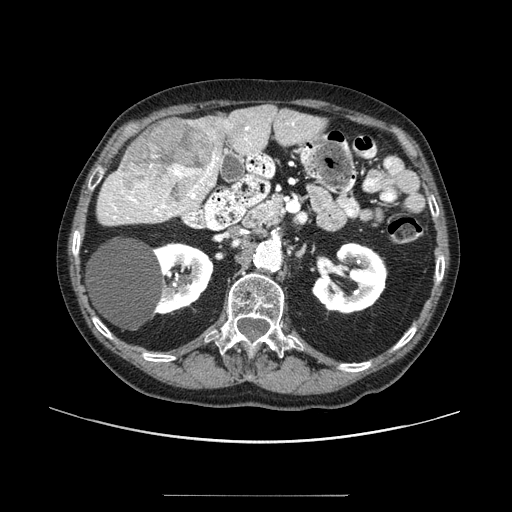
Contrast-enhanced abdominal CT (liver protocol), one axial slice; slice 41 of 91 in the series (ordered by position); reconstruction kernel STANDARD; 100 kVp; one of 2 acquisitions stored at this slice position; soft-tissue window (W 400 / L 40 HU); 2.5 mm slice thickness; 512 × 512 image matrix, field of view 400 × 400 mm. Case-level facts recorded for this patient, not image findings: diagnosis: hepatocellular carcinoma (patient treated with transarterial chemoembolisation; whether this scan precedes or follows treatment is not stated here); TNM stage (as recorded): Stage-I; Child-Pugh class: A.
Annotated regions visible in this slice (semi-automatic segmentation, software-assisted and operator-edited):
- liver parenchyma outside the tumour (the mass and vessels are separate outlines, so this box may not span the whole liver): bounding box [x1, y1, x2, y2] px = [98, 104, 326, 224]
- mass: [121, 120, 216, 206]
- liver vessels: [105, 123, 294, 219]